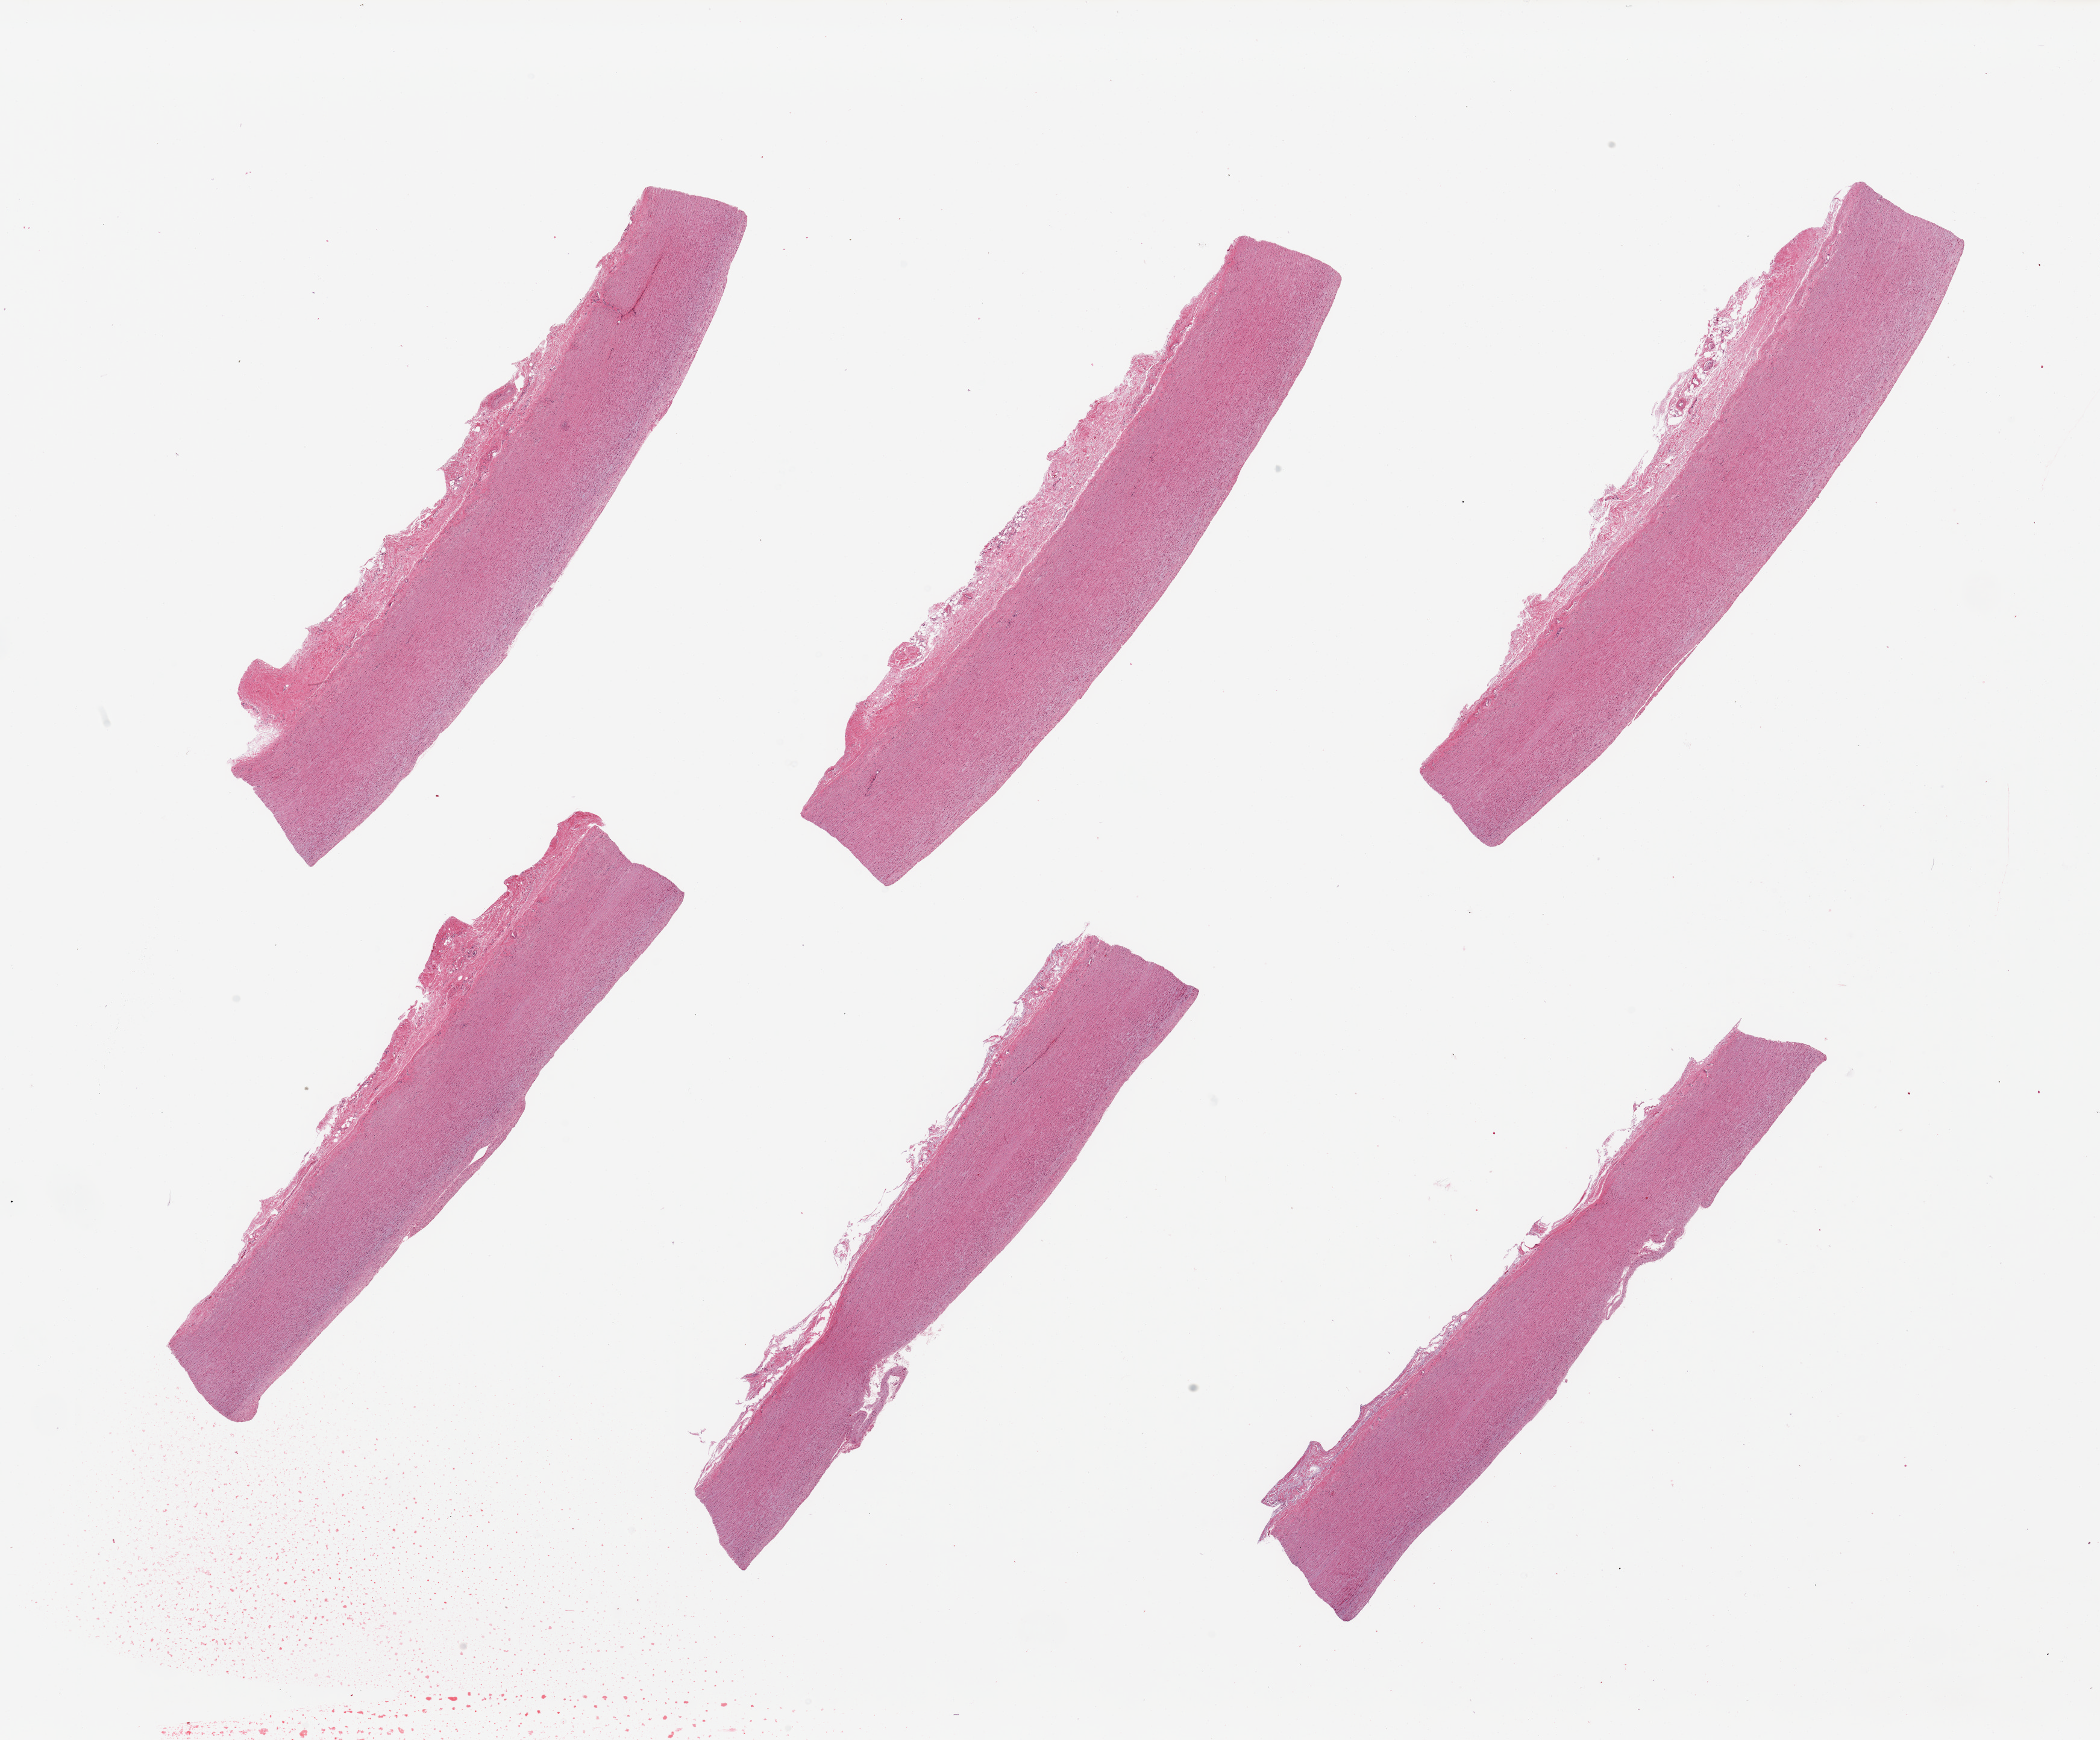
Whole-slide image, H&E stain, brightfield — a low-resolution overview of the entire scanned area, about 27.6 x 22.8 mm (acquisition: 20x scan). PAXgene-fixed paraffin-embedded (PFPE) section. Target tissue: aorta. Donor tissue sample. Donor sex: male.
Reviewer comment on this tissue sample: 6 pieces; up to 0.8mm attached adventitia.